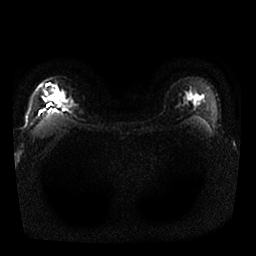
Breast MRI, one axial slice. Slice 20 of 25 in the series (ordered by position). Diffusion-weighted series; image 2 of 4 stored at this slice position (different b-values; order by instance number). 1.5 T. 4 mm slice thickness. 256 × 256 image matrix, field of view 340 × 340 mm. Female patient.
Annotated regions visible in this slice (expert manual segmentation):
- tumour on diffusion-weighted imaging: bounding box [x1, y1, x2, y2] px = [45, 92, 48, 95]